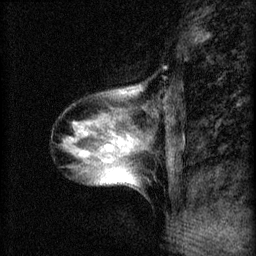
Breast MRI (dynamic contrast-enhanced), one sagittal slice. Slice 17 of 60 in the series (ordered by position). 3 images stored at this slice position (order not interpretable as contrast timing). 1.5 T. TE 4.2 ms, TR 8.2 ms. 2 mm slice thickness. 256 × 256 image matrix, field of view 180 × 180 mm. Female patient, age 40 years.
Outlined on this slice (semi-automatically segmented with operator editing):
- analysis volume of interest (the breast-tissue region the enhancement analysis was run in; not a lesion): box from (x=60, y=82) to (x=149, y=191) px
- tumour enhancement mask (voxels above the 70 % enhancement threshold inside the analysis volume of interest): (x=107, y=136)–(x=137, y=149)